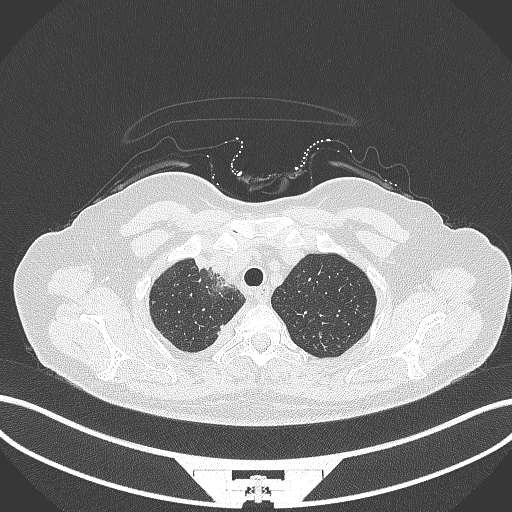
Chest CT, one axial slice; 120 kVp; lung window (W 1500 / L -600 HU); 1 mm slice thickness; 512 × 512 image matrix, field of view 400 × 400 mm. Female patient, age 52 years. From the clinical record (not read from this slice): clinical TNM (as recorded): T3 N1 M1.
Structures marked on this image (rectangle marked by the reading radiologist):
- lung tumour (recorded histology: adenocarcinoma): box from (x=189, y=253) to (x=216, y=274) px